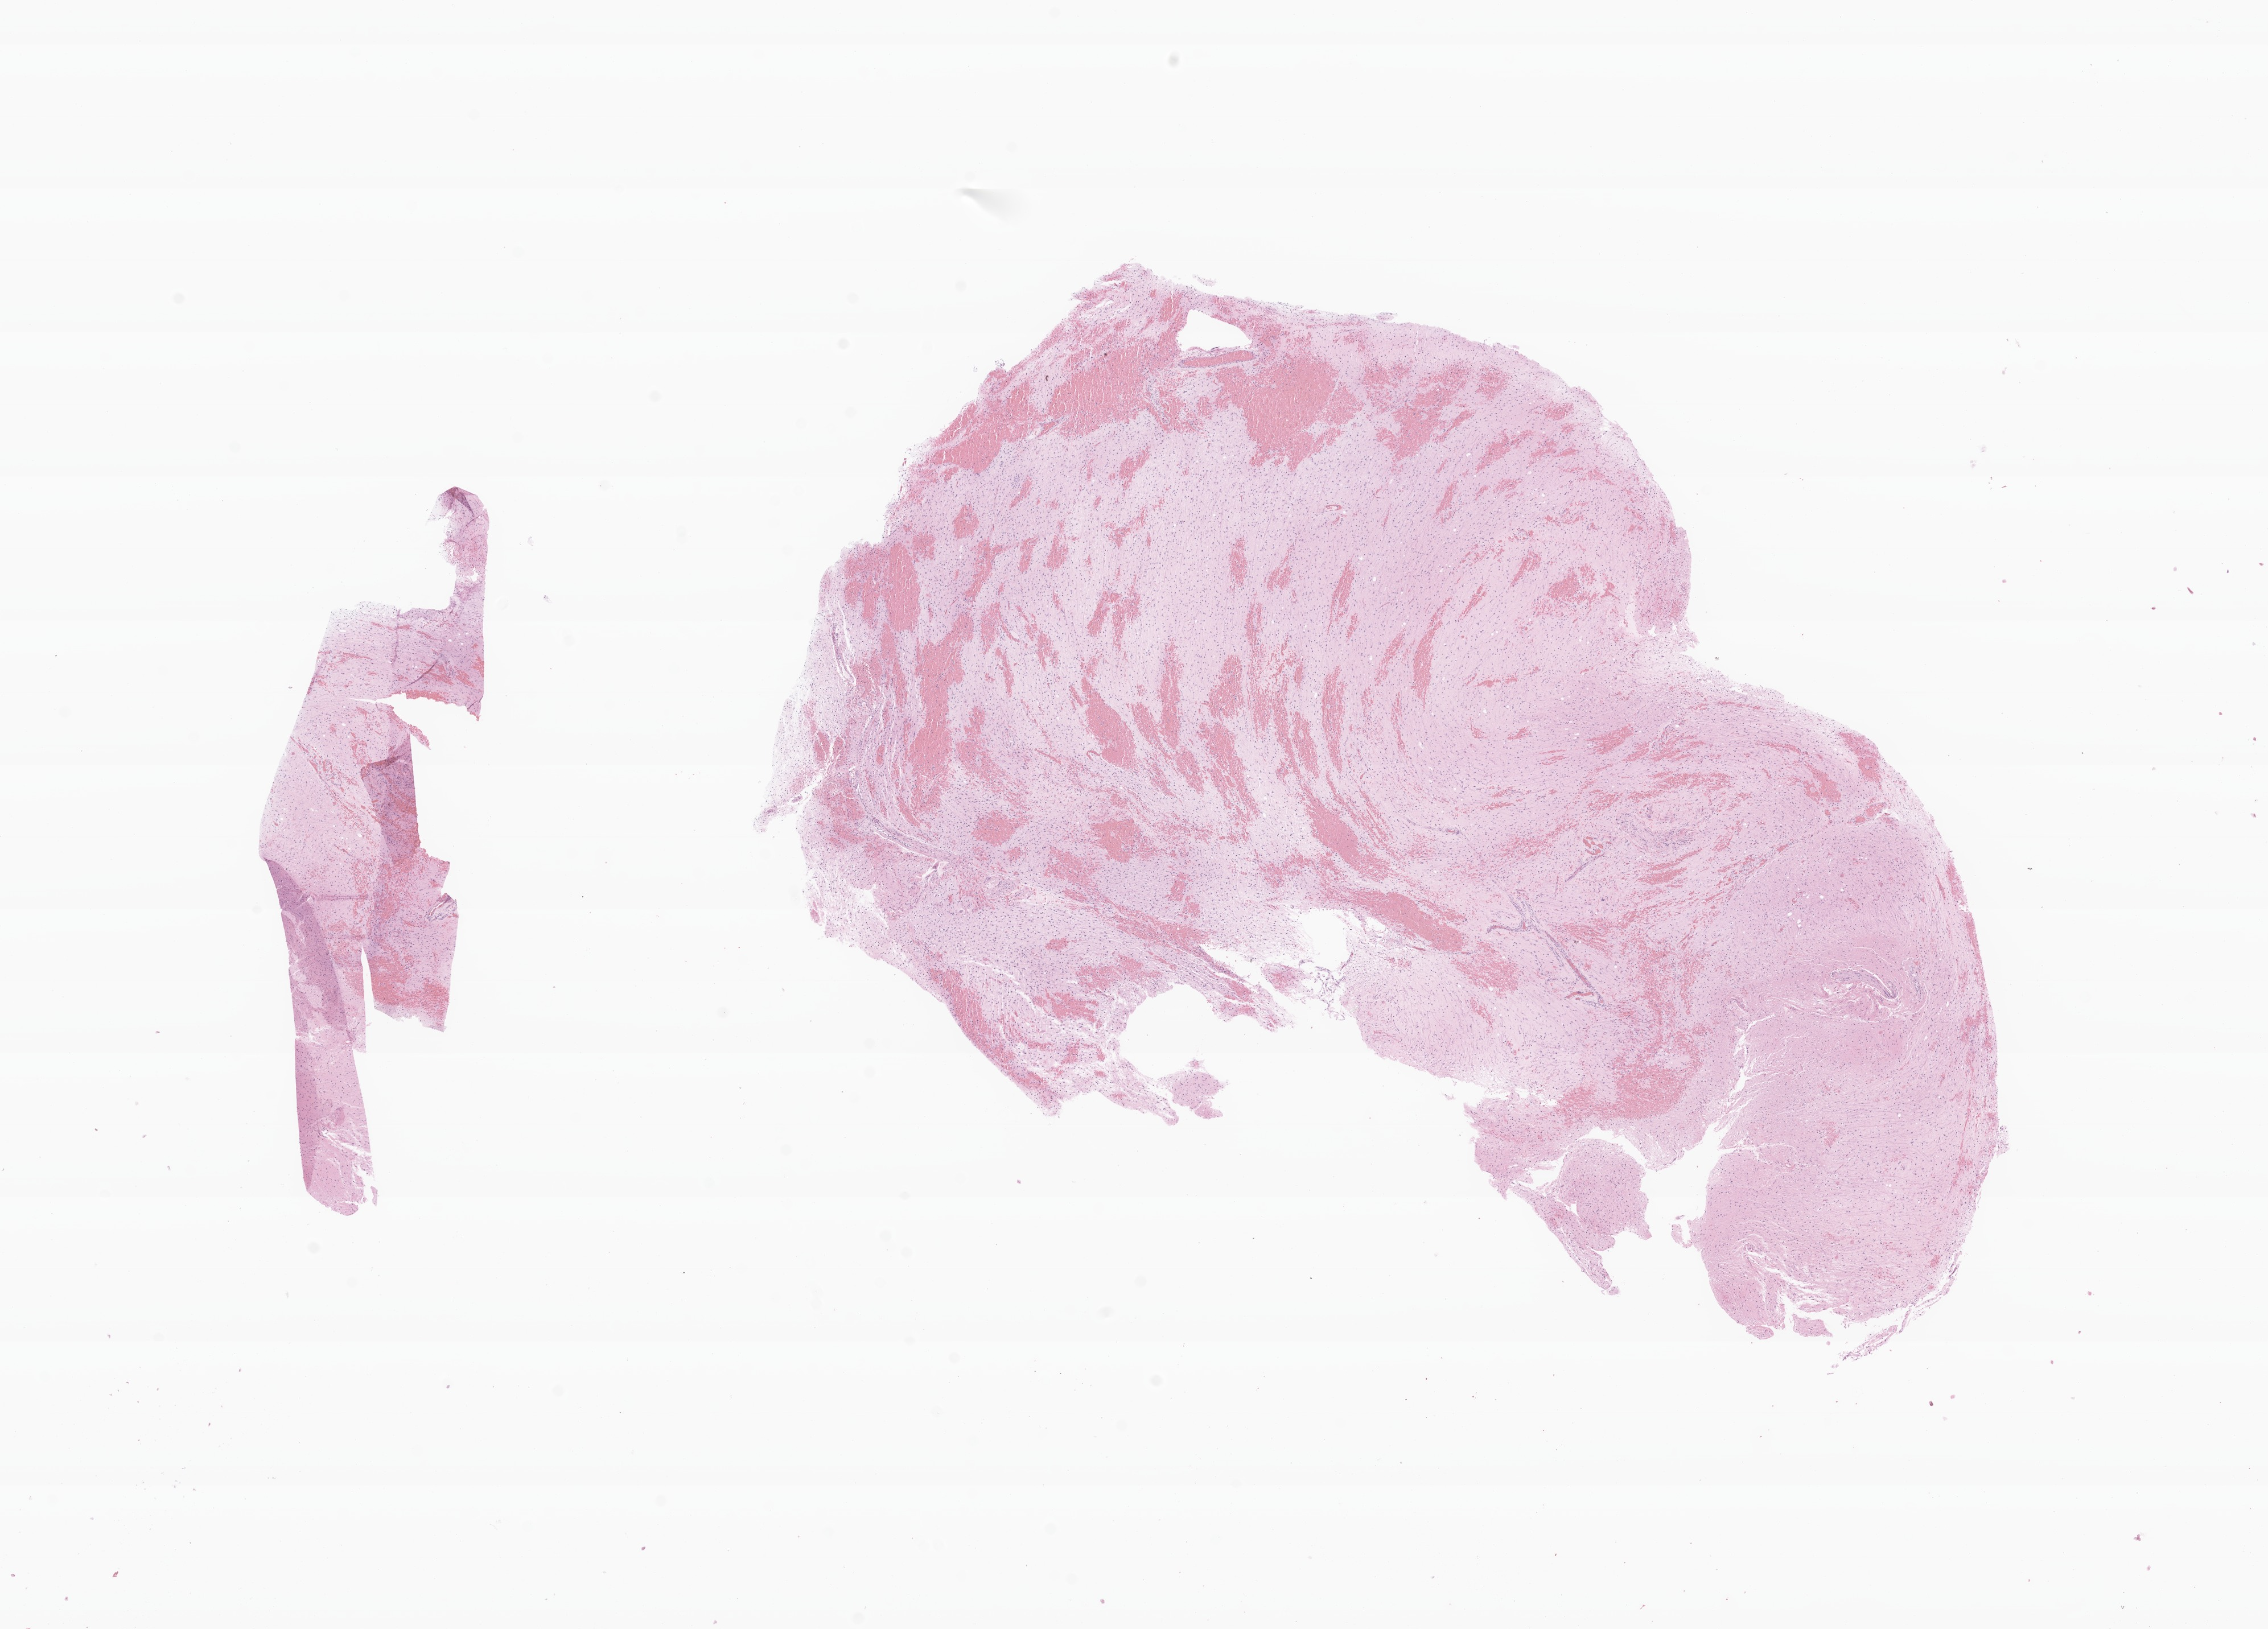
Digitized H&E-stained section of tumor tissue from the brain stem — whole scanned area (about 16.8 x 12.0 mm) shown as a low-resolution overview; formalin-fixed paraffin-embedded section. Patient: female, age 142 months (11 years 10 months).
Diagnosis: Pilocytic astrocytoma.